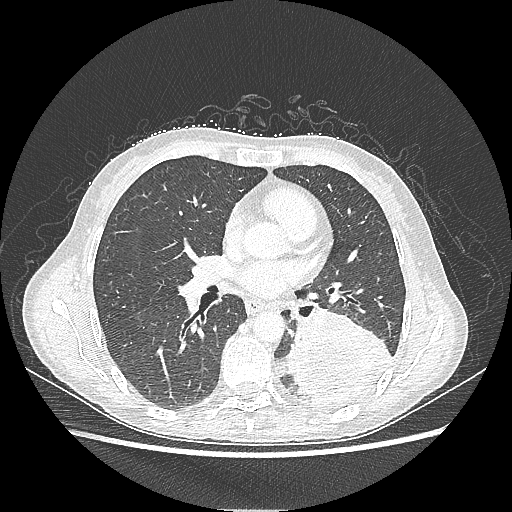
Chest CT, one axial slice. Slice 115 of 220 in the series (ordered by position). Reconstruction kernel LUNG. 80 kVp. Lung window (W 1500 / L -600 HU). 1.25 mm slice thickness. 512 × 512 image matrix, field of view 360 × 360 mm. Female patient, age 53 years. Case-level facts recorded for this patient, not image findings: clinical TNM (as recorded): T3 N0 M0.
Annotated regions visible in this slice (rectangle marked by the reading radiologist):
- lung tumour (recorded histology: adenocarcinoma): box from (x=283, y=307) to (x=394, y=411) px